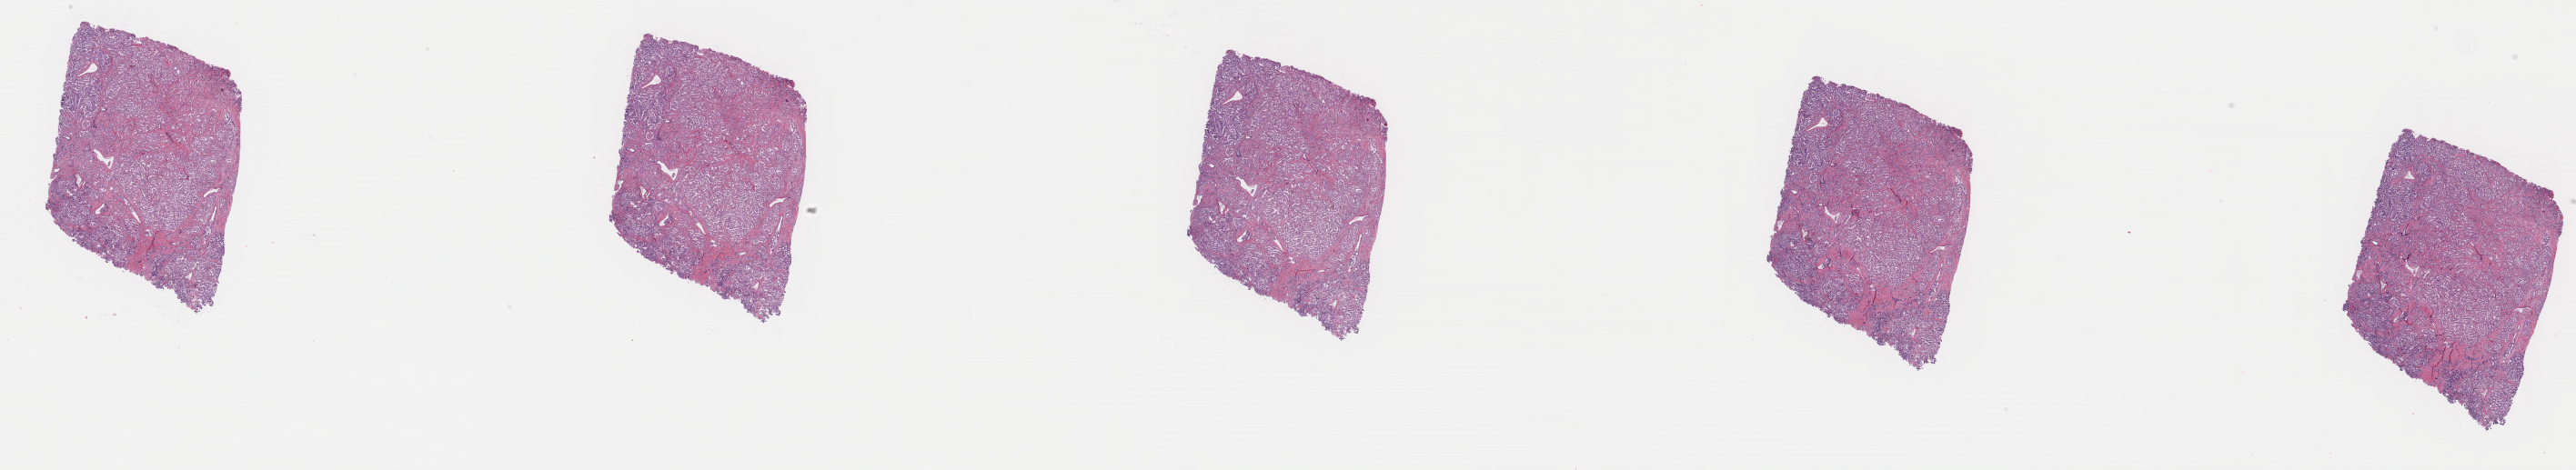
Whole-slide histology image, Hematoxylin and eosin (H&E) stained — a low-resolution overview of the entire scanned area, about 45.8 x 8.4 mm, formalin-fixed paraffin-embedded (FFPE) diagnostic section, prostate, primary tumour sample. Patient: male, age at initial diagnosis 56 years. Gleason score: 8 (4+4). Composition of this section per pathologist review: tumour cells 70%, tumour nuclei 80%, normal cells 0%, stromal cells 30%, necrosis 0%. Inflammatory infiltration, as recorded: lymphocyte infiltration 0%, monocyte infiltration 0%, neutrophil infiltration 0%.
Diagnosis: Adenocarcinoma, NOS (prostate gland). Lymph nodes positive (case pathology): 0 of 6 examined. Laterality: bilateral.